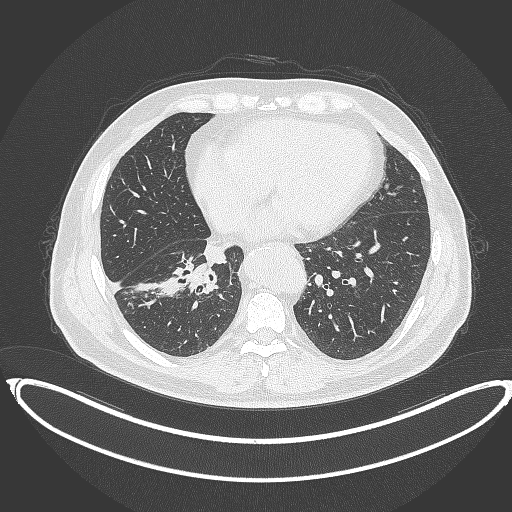
Chest CT, one axial slice. Position 150 of 387 along the scan axis. Reconstruction kernel B70f. 120 kVp. Lung window (W 1500 / L -600 HU). 1 mm slice thickness. 512 × 512 image matrix, field of view 448 × 448 mm. Patient: male, 61 years. Case-level facts recorded for this patient, not image findings: clinical TNM (as recorded): T1b N1 M0.
Outlined on this slice (rectangle marked by the reading radiologist):
- lung tumour (recorded histology: squamous cell carcinoma): box from (x=157, y=253) to (x=219, y=300) px